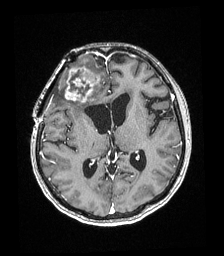
Brain MRI from a brain-tumour surgery series, one axial slice. T1-weighted post-contrast. 1 mm slice thickness. 224 × 256 image matrix. From the clinical record (not read from this slice): histopathology: Astrocytoma; WHO grade: 4; IDH mutation: yes.
Annotated regions visible in this slice (outlined manually by an expert reader):
- tumour: bounding box (x1, y1, x2, y2) in pixels: (65, 59, 100, 102)